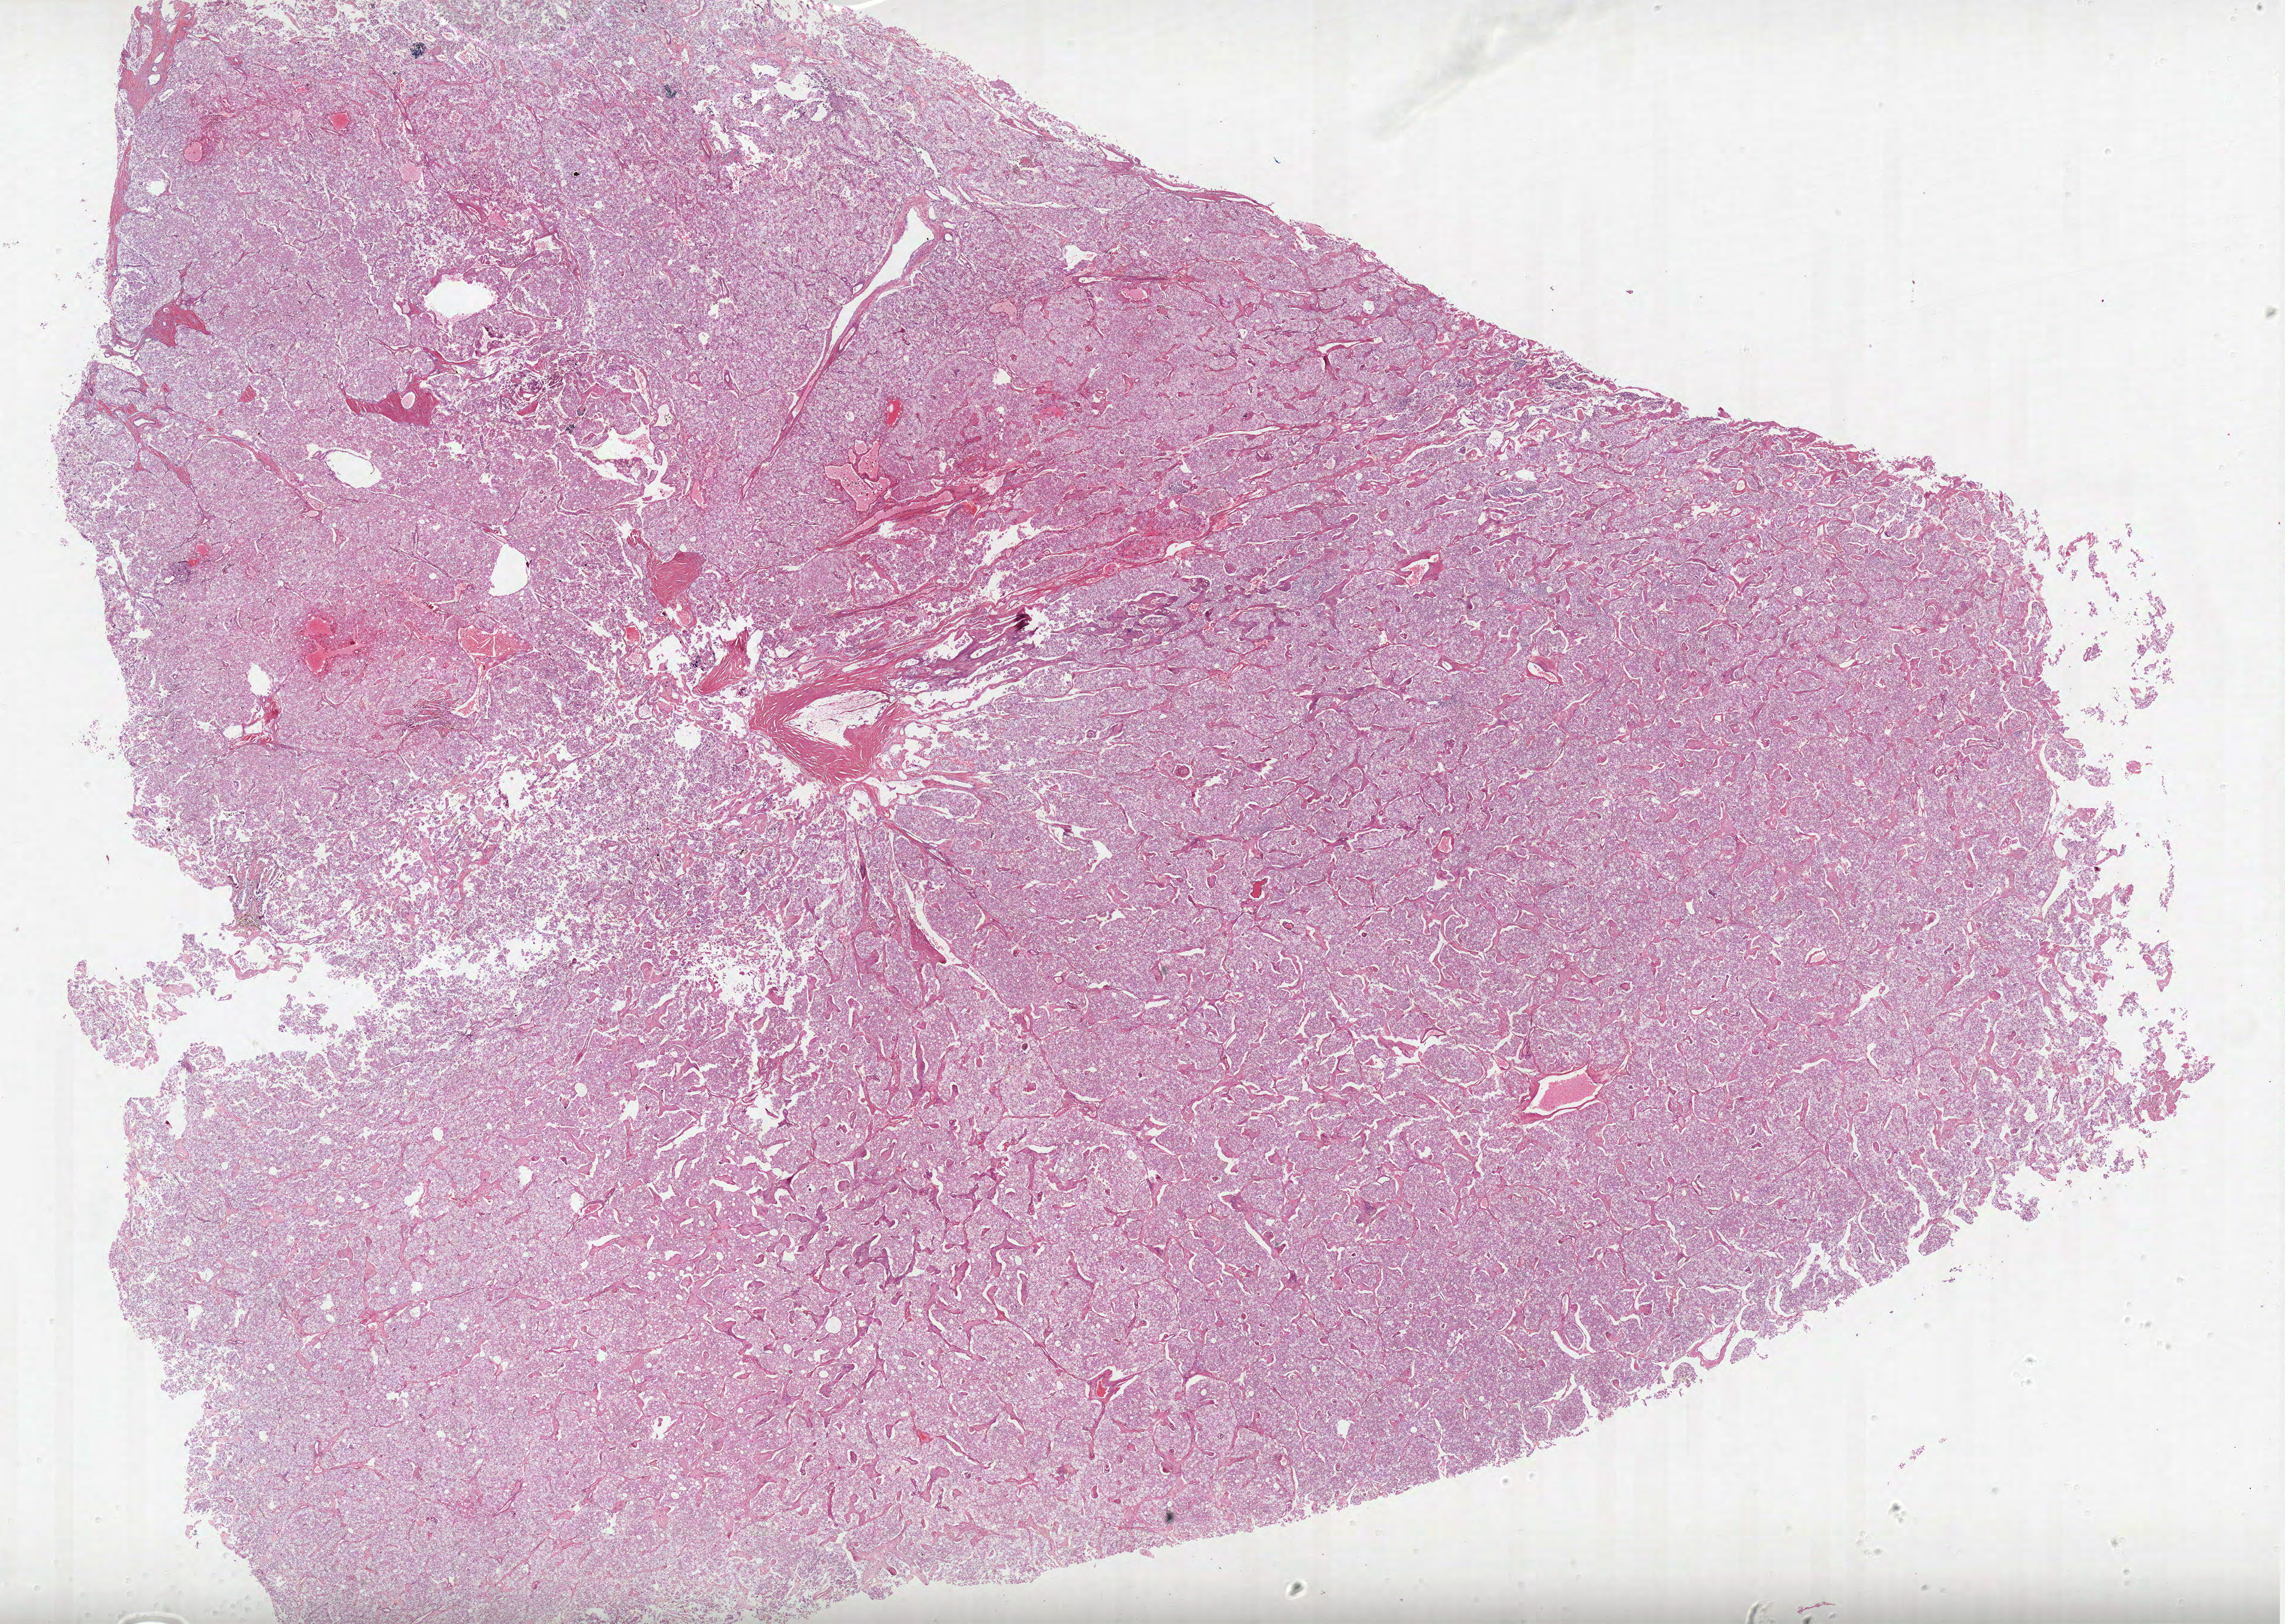
Digitized H&E-stained tissue section (whole slide) — shown as a low-resolution overview of the whole scanned area (about 30.4 x 21.6 mm), formalin-fixed paraffin-embedded (FFPE) diagnostic section, kidney, primary tumour sample. Patient: male, age at initial diagnosis 56 years. Histologic grade: G3 (poorly differentiated).
AJCC pathologic stage: III. Histologic diagnosis: Clear cell adenocarcinoma, NOS.